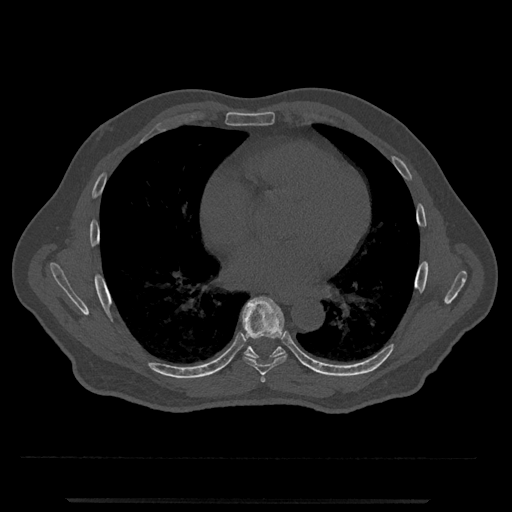
CT including the spine, one axial slice; position 662 of 797 along the scan axis; reconstruction kernel Br40s/3; 120 kVp; bone window (W 1800 / L 400 HU); 0.5 mm slice thickness; 512 × 512 image matrix, field of view 419 × 419 mm. Patient: male, 63 years. From the clinical record (not read from this slice): primary cancer: prostate.
Structures marked on this image (semi-automatically segmented with operator editing):
- T6 vertebra: box from (x=260, y=375) to (x=266, y=383) px
- T7 vertebra: (x=242, y=296)–(x=288, y=375)
- T8 vertebra: (x=244, y=338)–(x=285, y=359)